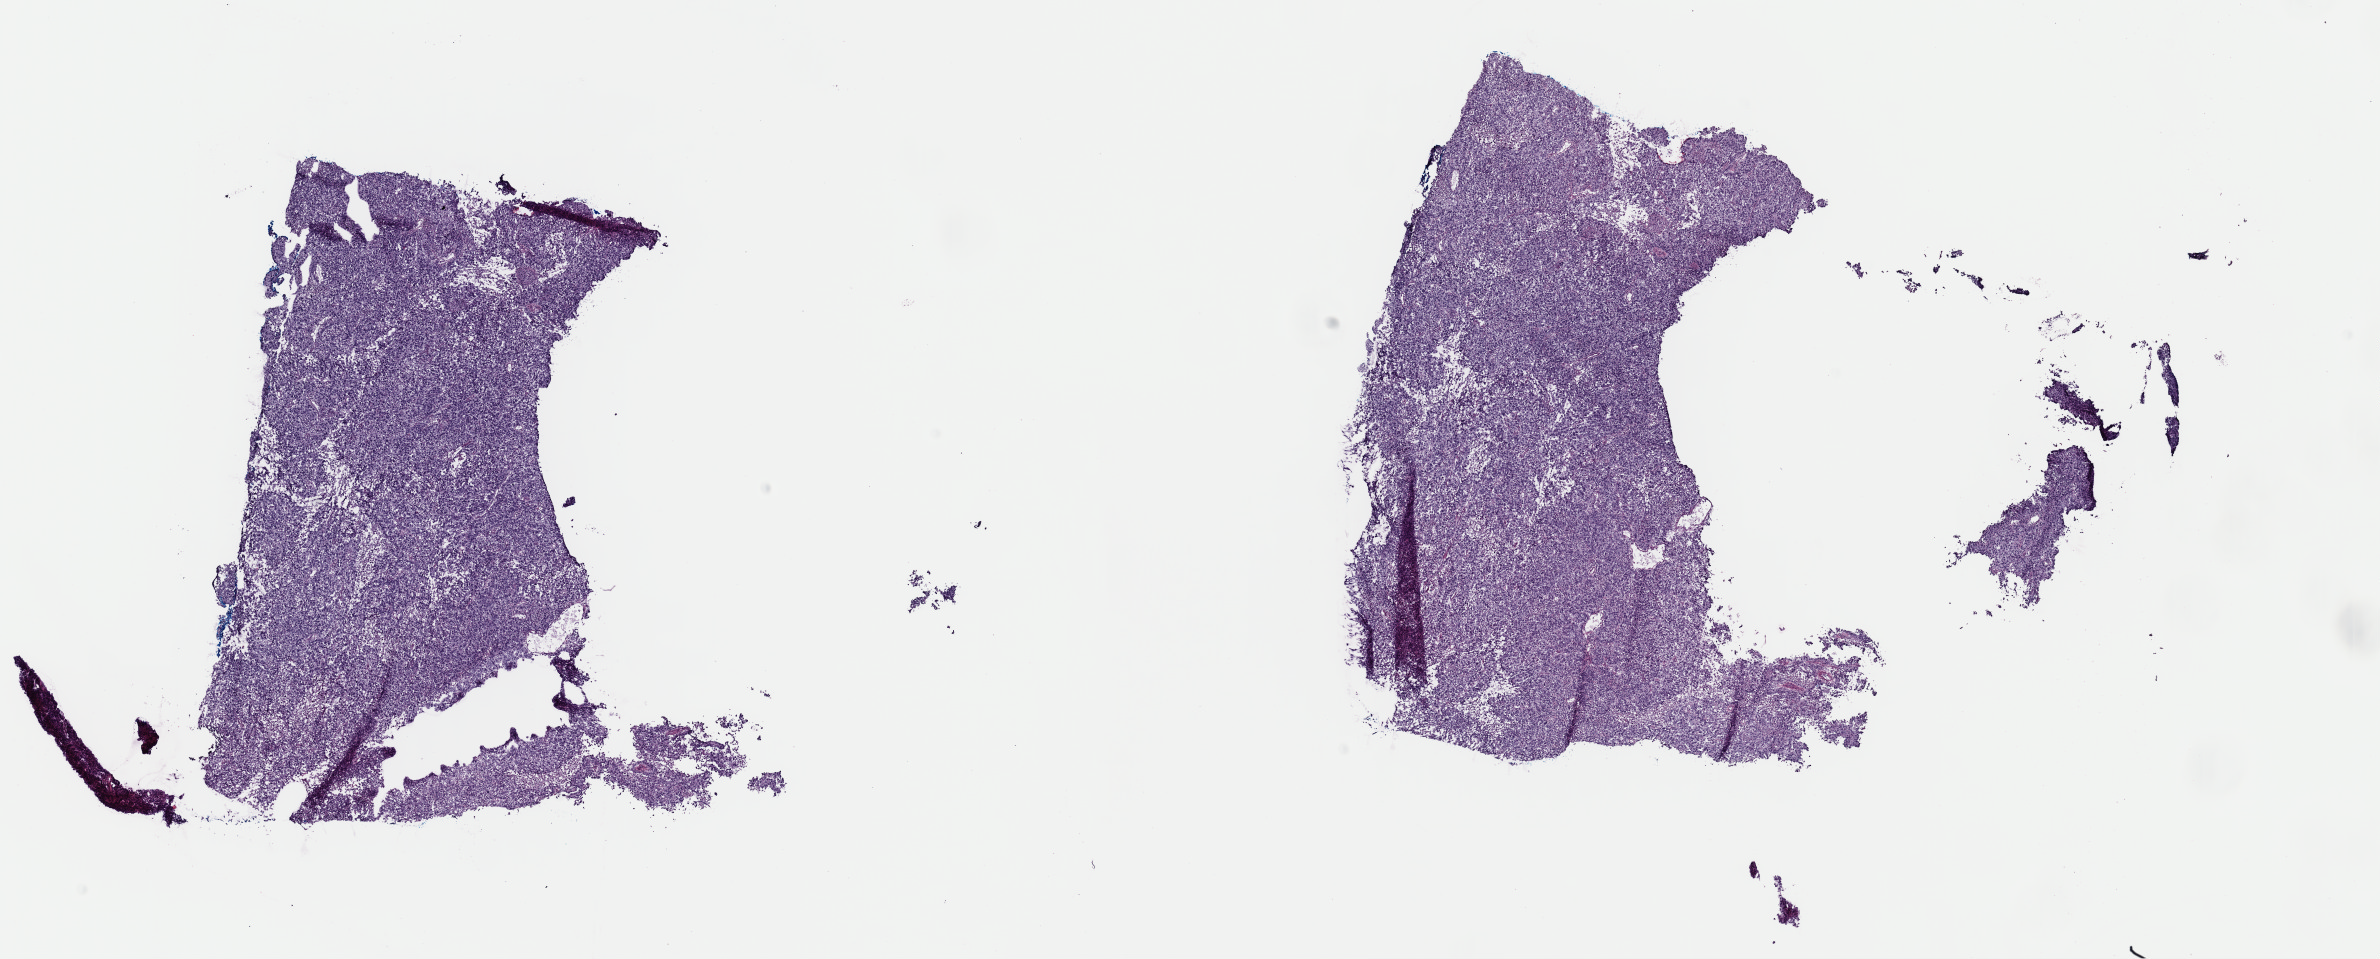
Digitized Hematoxylin and eosin (H&E) stained tissue section (whole slide), a low-resolution overview of the entire scanned area, about 18.8 x 7.6 mm (from a 40x scan); frozen section; sample: primary tumour, uterus. Female patient; age at initial diagnosis 78 years. Histologic grade: G3 (poorly differentiated). Pathologist review of this section (percent, as recorded): tumour cells 95%, tumour nuclei 90%, normal cells 0%, stromal cells 0%, necrosis 5%. Inflammatory infiltration, as recorded: lymphocyte infiltration 3%, monocyte infiltration 1%, neutrophil infiltration 0%.
• FIGO stage: IB
• pathologic diagnosis: Serous cystadenocarcinoma, NOS (endometrium)